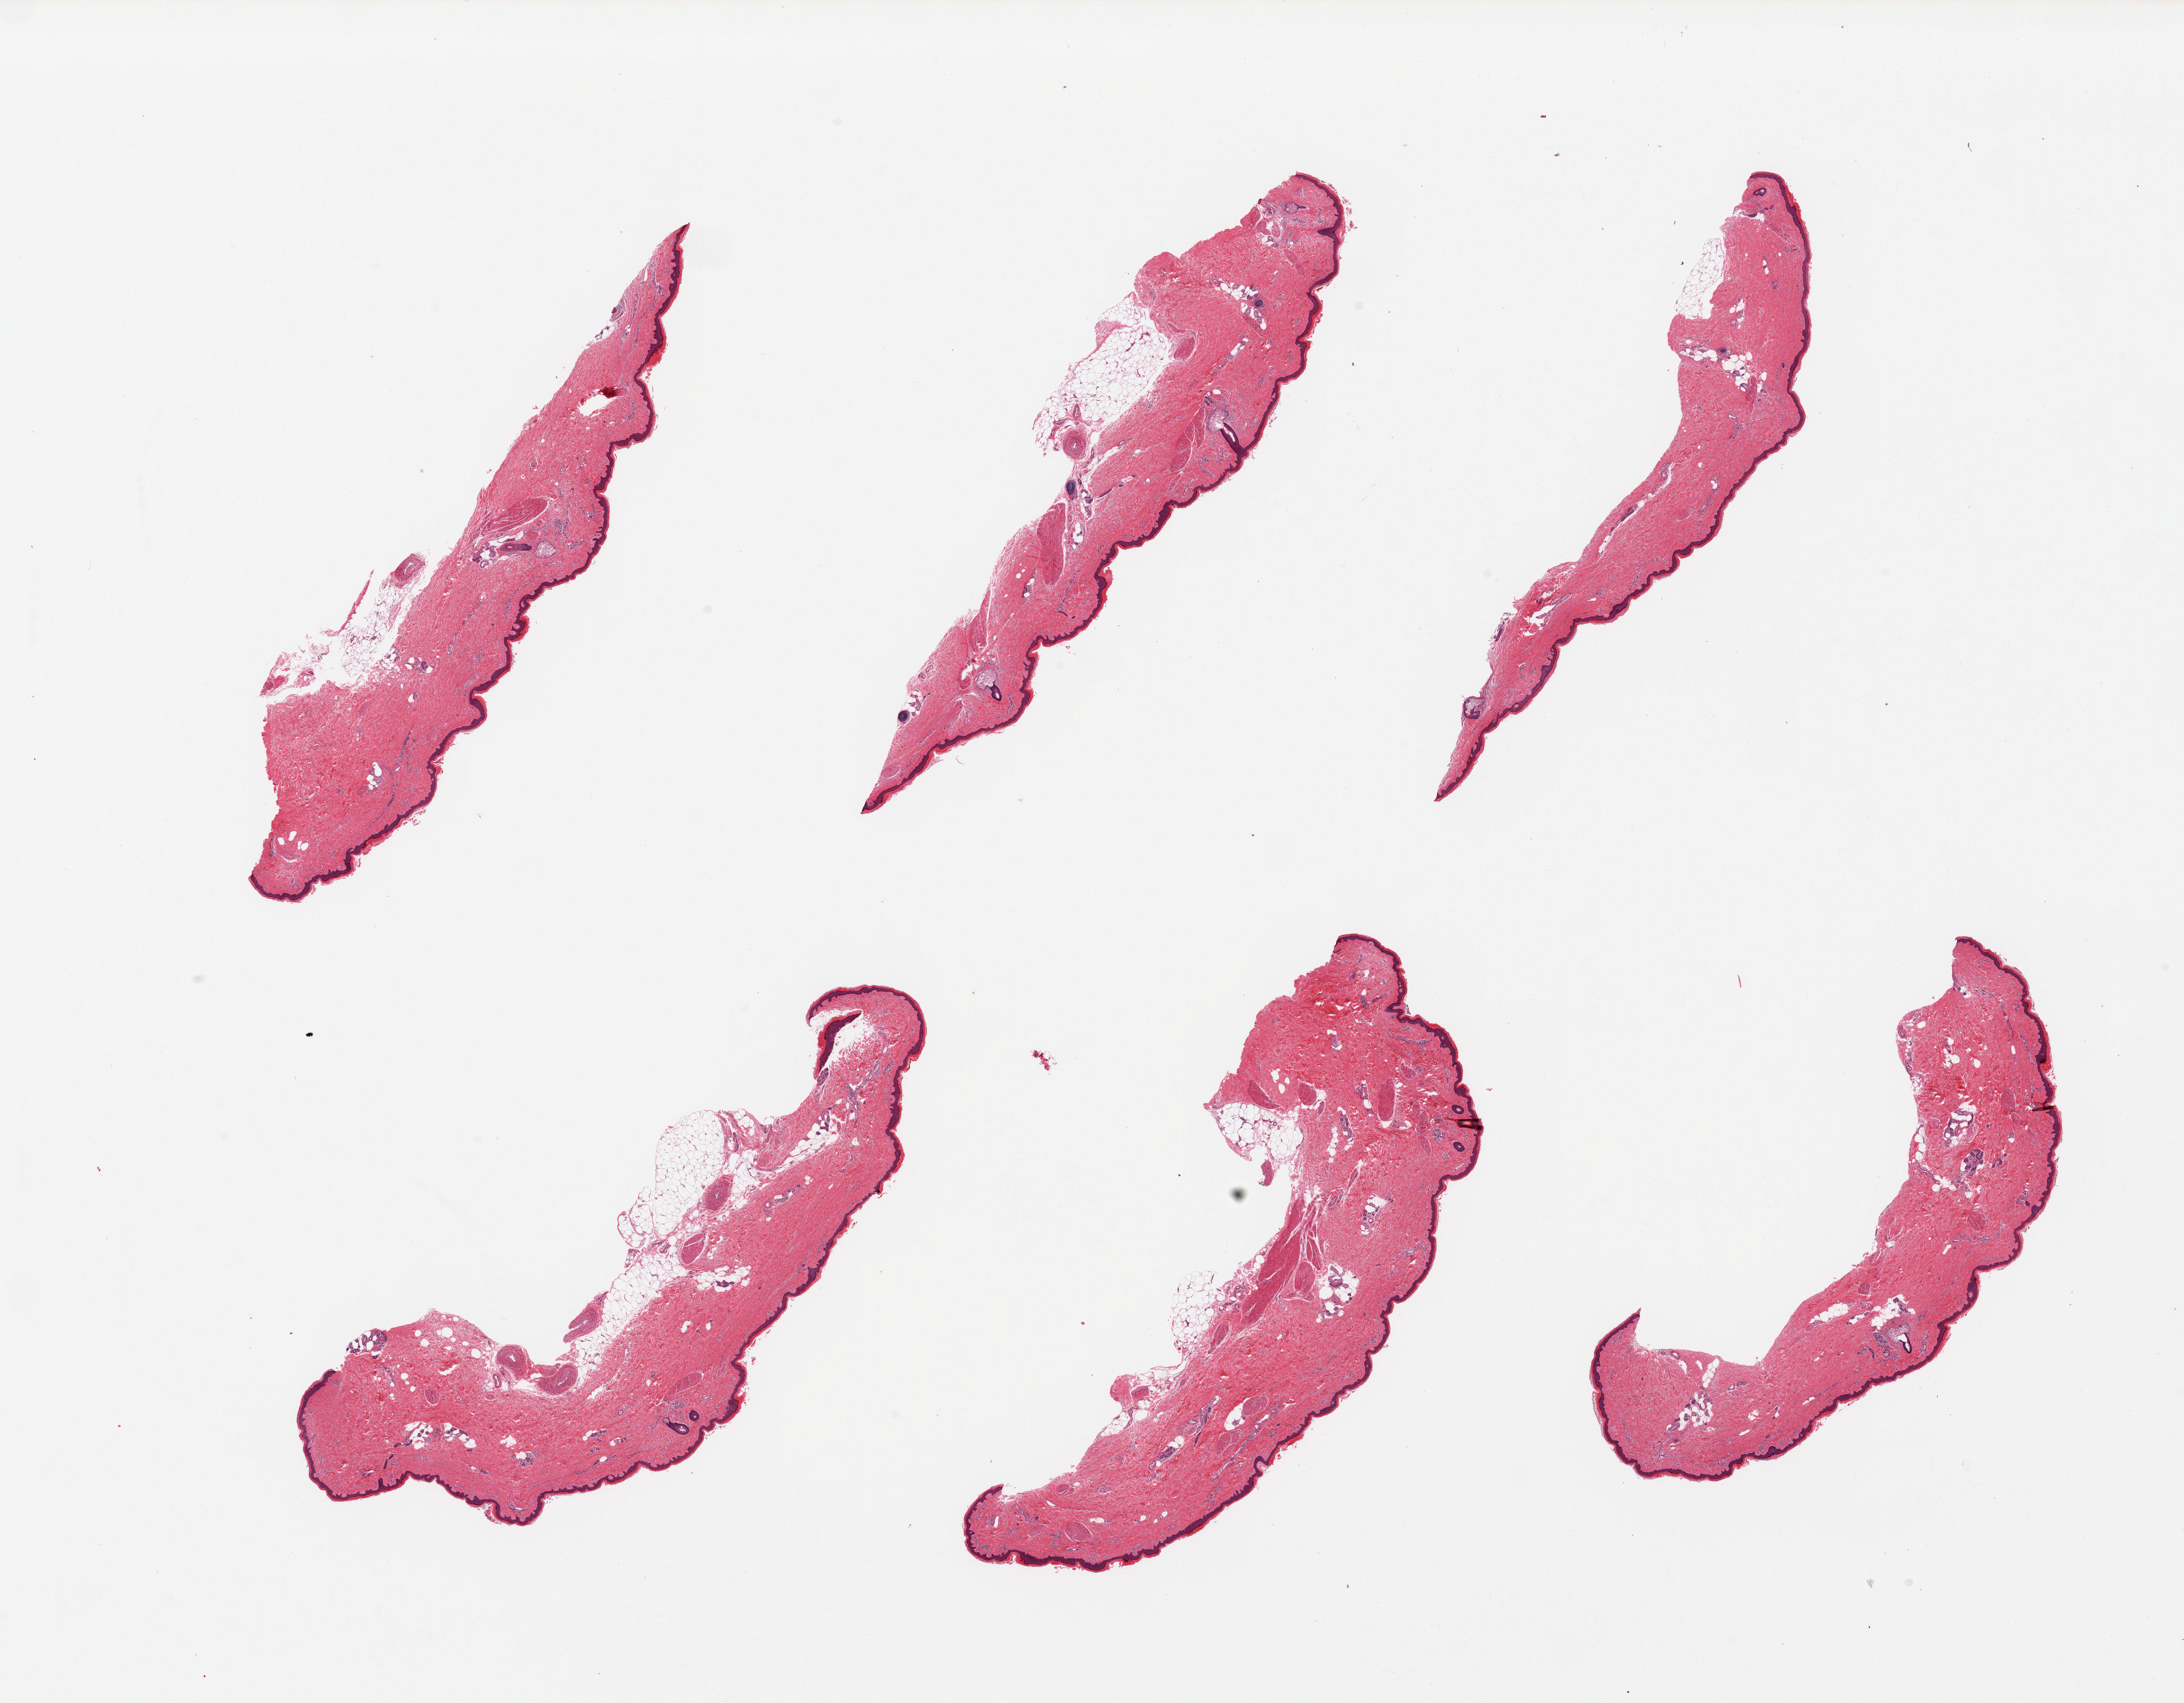
Digitized H&E-stained section, shown as a low-resolution overview of the whole scanned area (about 27.6 x 21.5 mm, acquisition: 20x scan). PAXgene-fixed paraffin-embedded (PFPE) section. Target tissue: skin of lower leg. Tissue donor sample.
- review note (as recorded): 1 piece skin, as with 2625